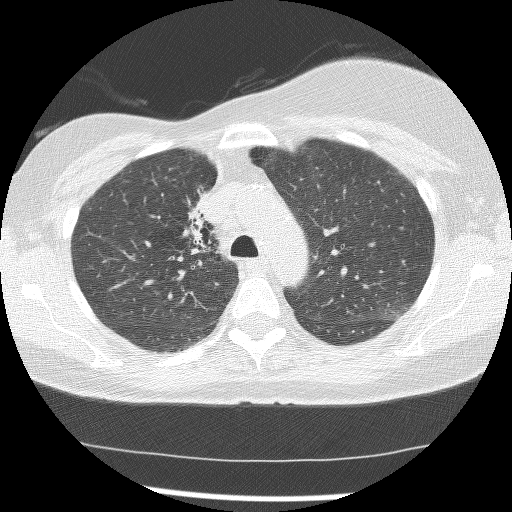
Chest CT (low-dose screening protocol), one axial image, first (baseline) screen, lung window (W 1500 / L -600 HU), 2.5 mm slice thickness, 120 kVp. Female participant, aged 56 years at enrolment. Current smoker at enrolment.
- Lesion marked by an expert reader, bounding box (x1, y1, x2, y2) in pixels: (164, 185, 221, 270).
- The screening reader recorded 2 non-calcified nodules or masses ≥4 mm on this exam (right lower lobe, right middle lobe); which of them this box marks is not recorded.